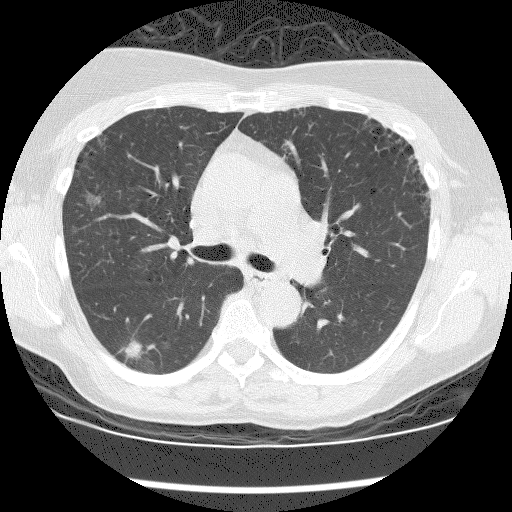
Low-dose screening chest CT, axial slice. First (baseline) screen. Lung window (W 1500 / L -600 HU). 2.5 mm slice thickness. Female, age 59 years at enrolment. Current smoker at enrolment.
Expert reader's lesion annotation, box from (x=110, y=339) to (x=149, y=372) px. The screening reader recorded 6 non-calcified nodules or masses ≥4 mm on this exam (right upper lobe, right upper lobe, right lower lobe, right lower lobe, right upper lobe, right upper lobe); which of them this box marks is not recorded. Later outcome: lung cancer diagnosed 242 days after this screen — adenocarcinoma, NOS, right lower lobe, moderately differentiated (G2), stage IIIA (AJCC 6th edition), 12 mm at pathology.